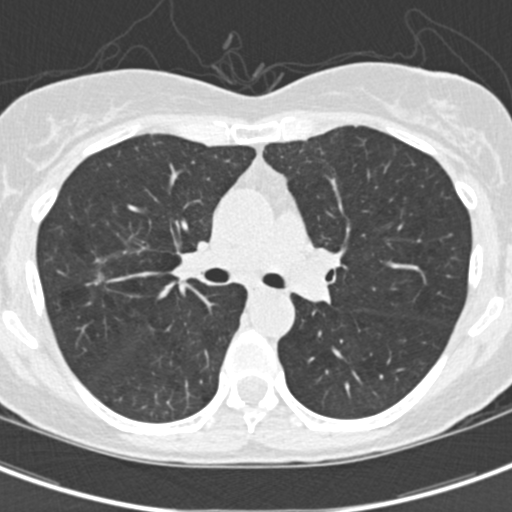
Low-dose screening chest CT, one axial slice. Lung window (W 1500 / L -600 HU). 2 mm slice thickness. 512 × 512 image matrix.
Structures marked on this image (manually delineated by an expert):
- lesion 1 (tumor, upper lobe of right lung): bounding box <94,274,102,285> (left, top, right, bottom; pixels)